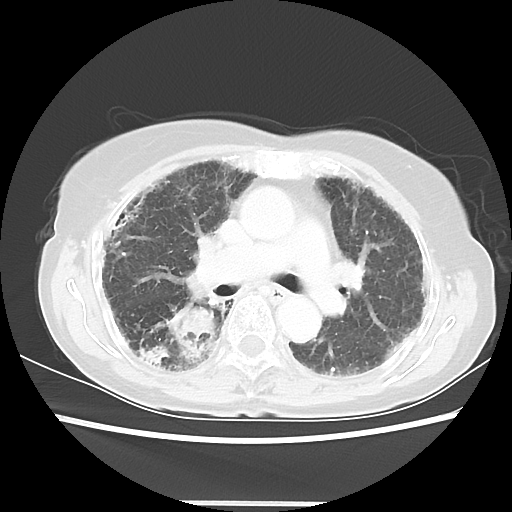
Chest CT, one axial slice; position 32 of 52 along the scan axis; lung window (W 1500 / L -600 HU); 5 mm slice thickness; 512 × 512 image matrix, field of view 325 × 325 mm. Patient: female, 71 years. From the clinical record (not read from this slice): clinical TNM (as recorded): T3 N0 M0.
Annotated regions visible in this slice (rectangle marked by the reading radiologist):
- lung tumour (recorded histology: squamous cell carcinoma): box from (x=161, y=300) to (x=217, y=358) px